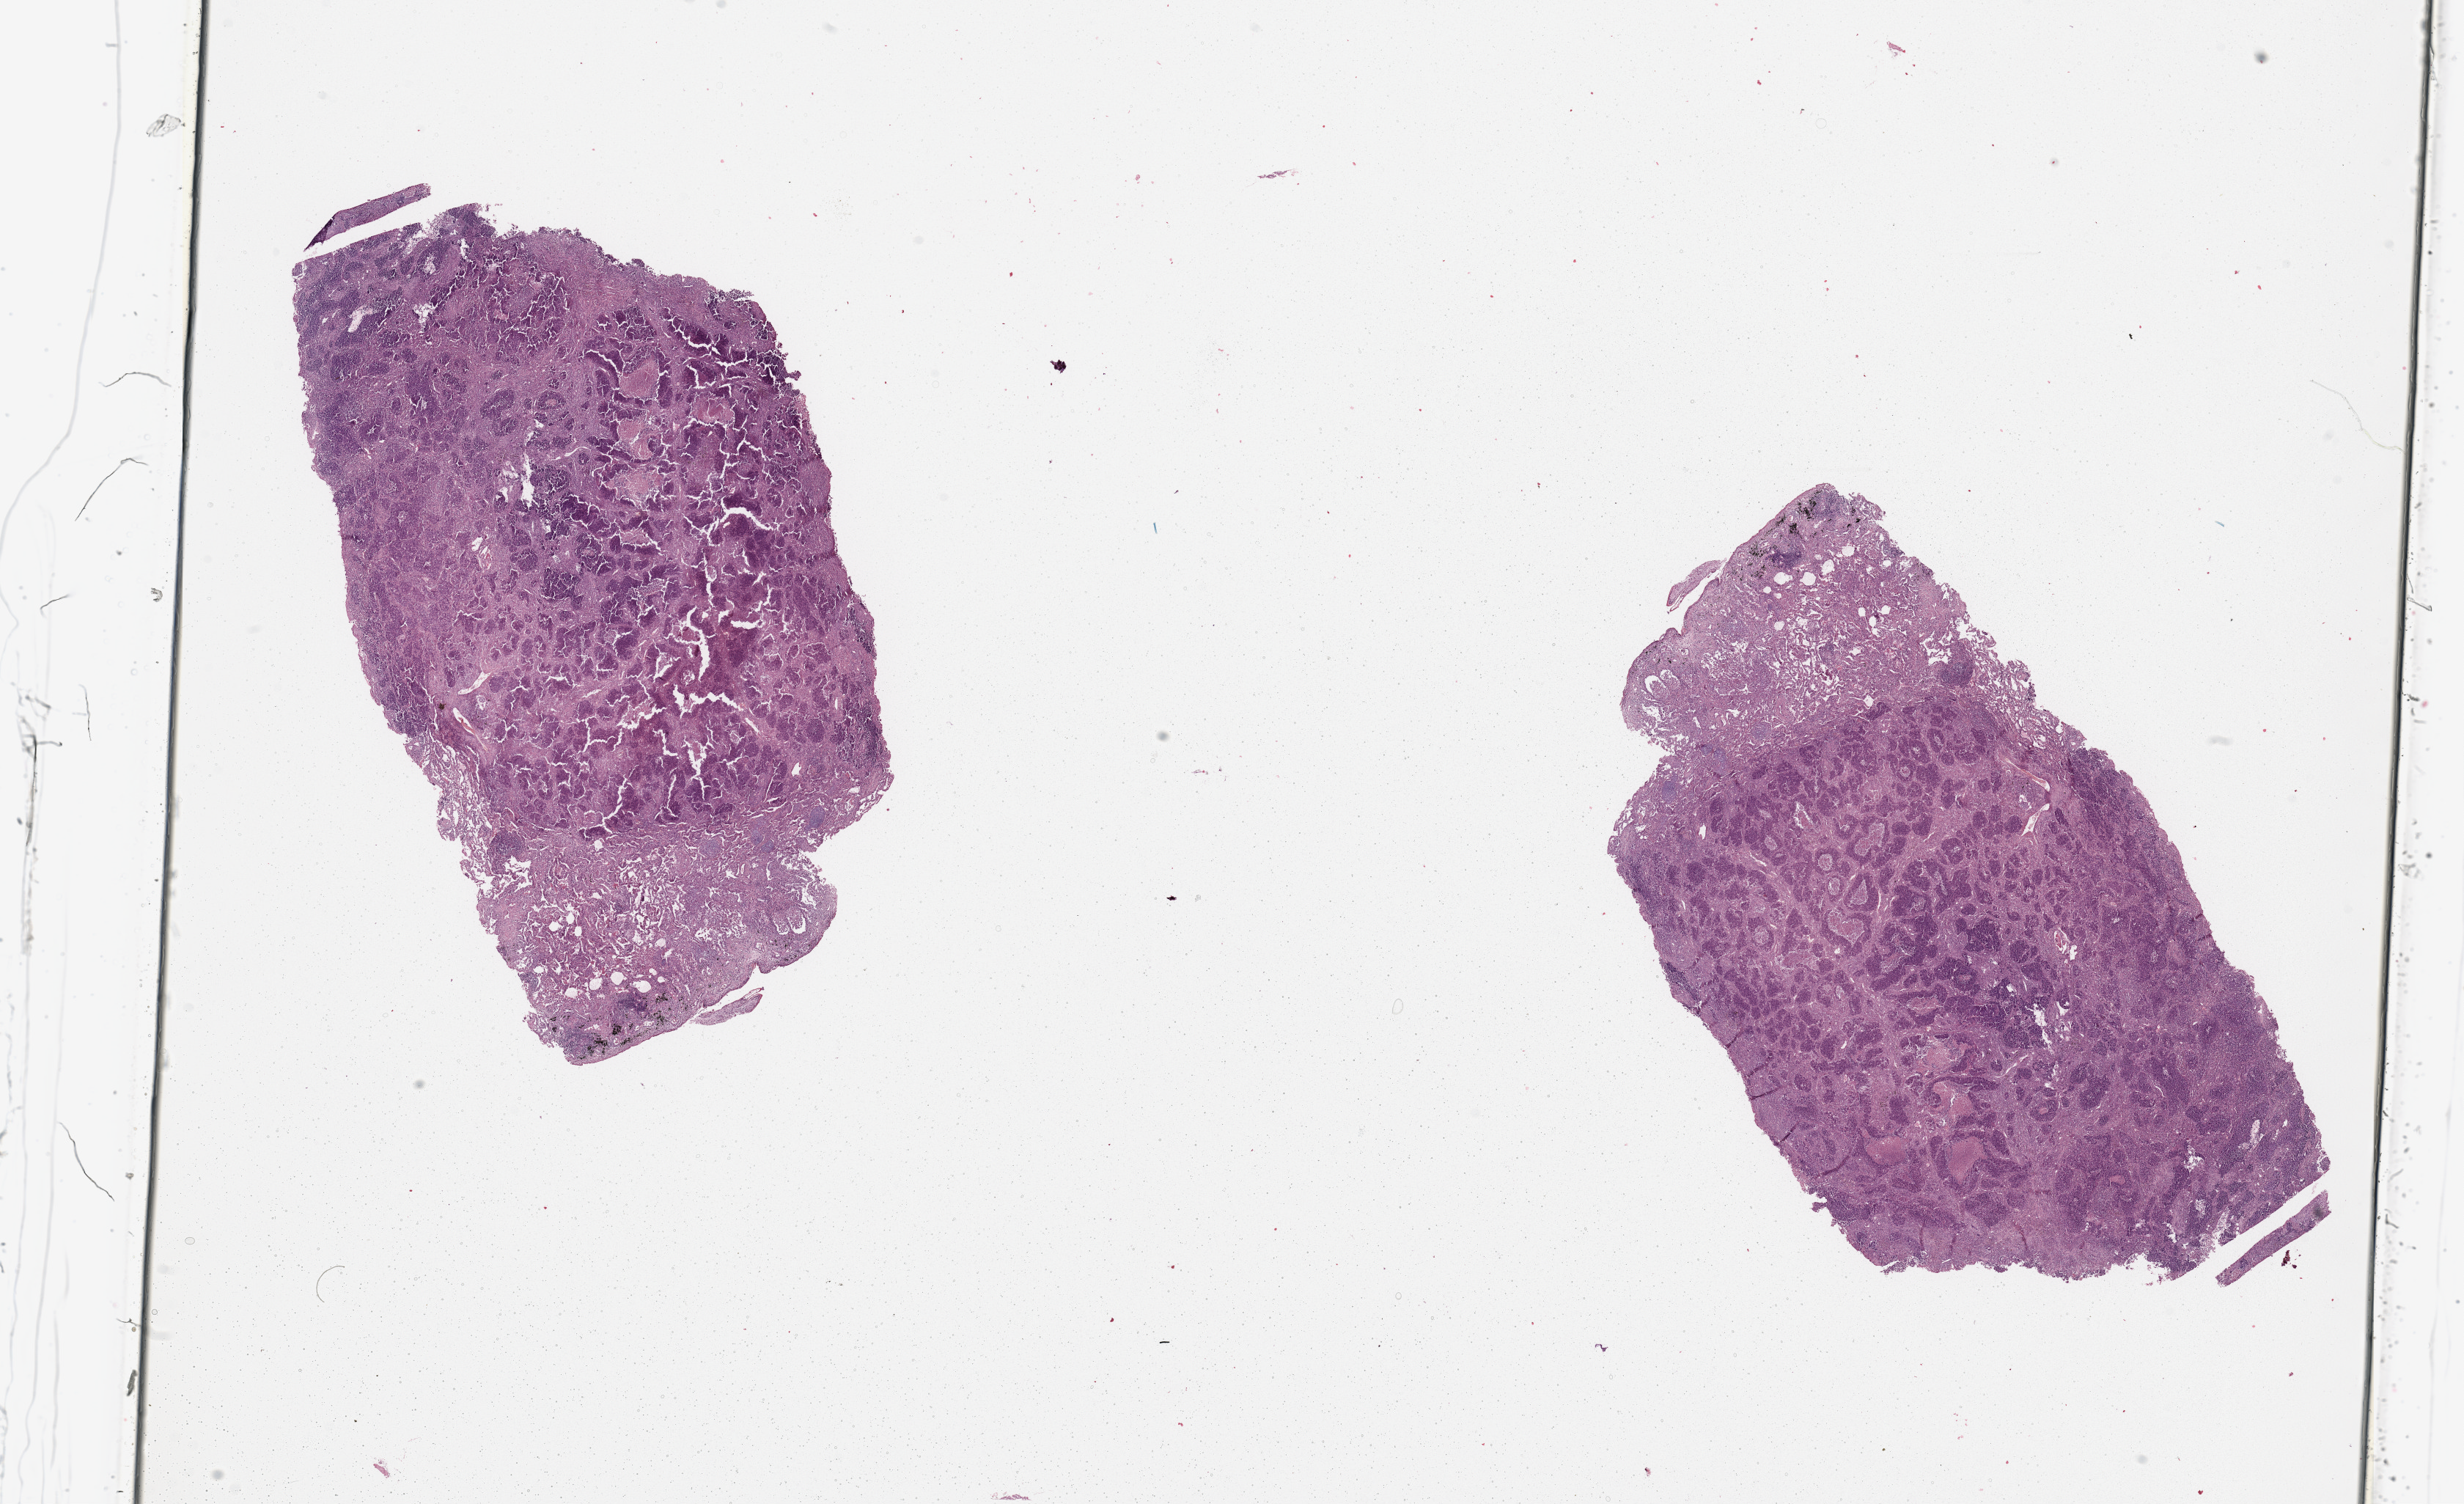
Digitized H&E-stained tissue section (whole slide), low-resolution overview of the scanned area, about 26.6 x 16.2 mm (slide scanned at 20x), tumour tissue sample, sampled site: lung. Patient: male, age 60 years. Histologic grade: GX (grade cannot be assessed). Pathologist review of this section (percent, as recorded): tumour nuclei 65%, necrosis 10%.
Histologic diagnosis: Squamous cell carcinoma, NOS. Primary tumour site (as recorded): left lower lobe. AJCC pathologic stage: IB.